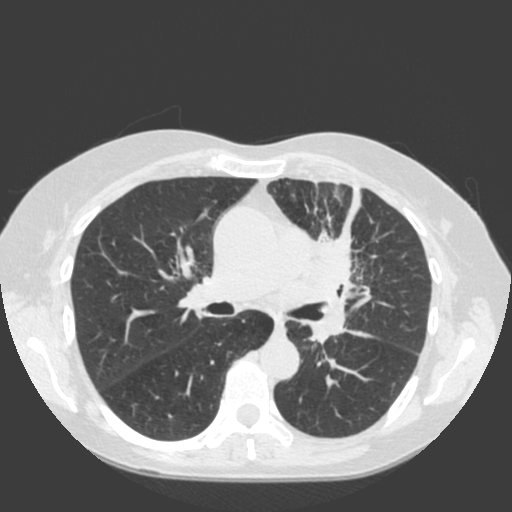
Low-dose screening chest CT, one axial slice. Position 114 of 184 along the scan axis. Lung window (W 1500 / L -600 HU). 512 × 512 image matrix, field of view 350 × 350 mm.
Annotated regions visible in this slice (manually delineated by an expert):
- lesion 1 (tumor, hilum of left lung): bounding box (x1, y1, x2, y2) in pixels: (300, 231, 370, 345)